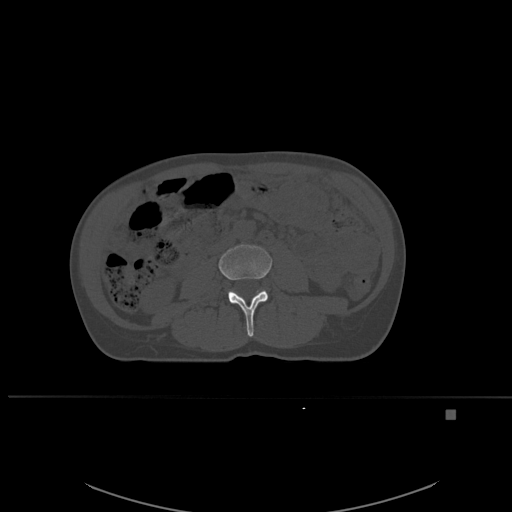
CT including the spine, one axial slice. Slice 209 of 537 in the series (ordered by position). Bone window (W 1800 / L 400 HU). 512 × 512 image matrix, field of view 440 × 440 mm. Patient: female, 45 years. Case-level facts recorded for this patient, not image findings: primary cancer: lung.
Outlined on this slice (semi-automatic segmentation, software-assisted and operator-edited):
- L3 vertebra: bounding box [x1, y1, x2, y2] px = [219, 244, 272, 337]
- L4 vertebra: [228, 290, 233, 297]